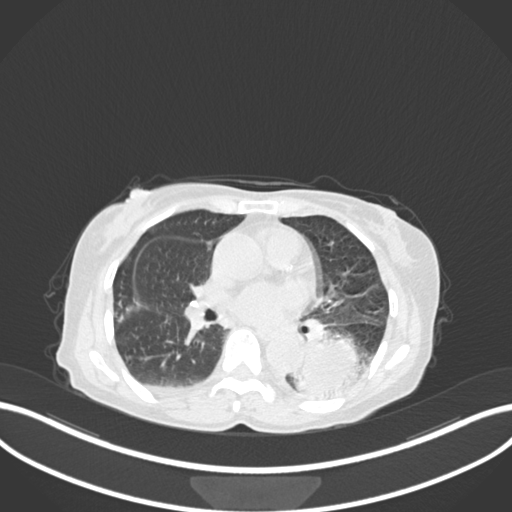
Chest CT, one axial slice; slice 80 of 233 in the series (ordered by position); reconstruction kernel B30f; 120 kVp; lung window (W 1500 / L -600 HU); 512 × 512 image matrix, field of view 400 × 400 mm. Female patient, age 78 years. From the clinical record (not read from this slice): clinical TNM (as recorded): T3 N0 M1.
Annotated regions visible in this slice (bounding box drawn by a radiologist):
- lung tumour (recorded histology: squamous cell carcinoma): bounding box <291,328,364,401> (left, top, right, bottom; pixels)